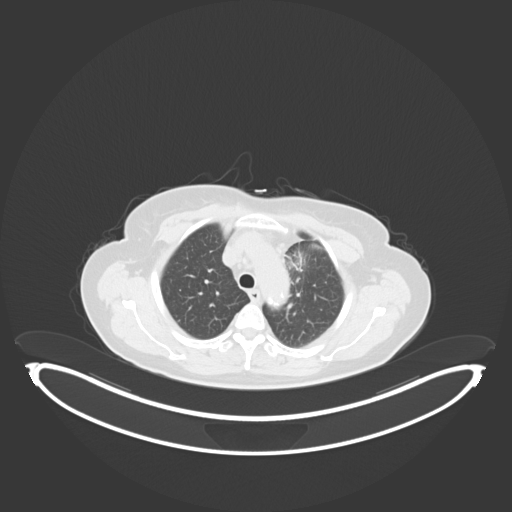
Chest CT, one axial slice. Position 197 of 243 along the scan axis. Lung window (W 1500 / L -600 HU). 3 mm slice thickness. 512 × 512 image matrix, field of view 500 × 500 mm. Female patient, age 65 years. From the clinical record (not read from this slice): clinical TNM (as recorded): T2a N0 M0.
Annotated regions visible in this slice (rectangle marked by the reading radiologist):
- lung tumour (recorded histology: adenocarcinoma): box from (x=284, y=248) to (x=307, y=274) px